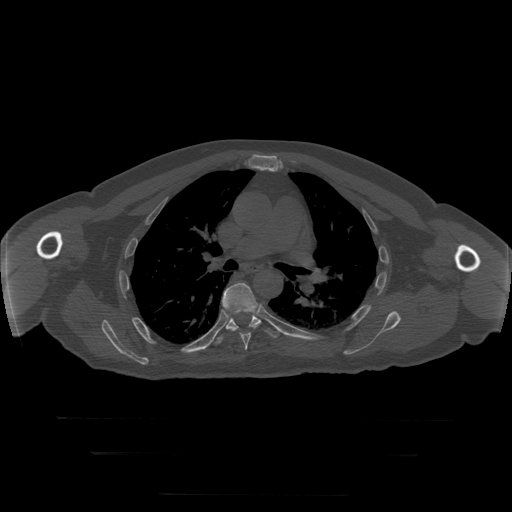
CT including the spine, one axial slice. Reconstruction kernel STANDARD. 120 kVp. Bone window (W 1800 / L 400 HU). 1.25 mm slice thickness. 512 × 512 image matrix. Patient age 73 years. From the clinical record (not read from this slice): primary cancer: prostate.
Annotated regions visible in this slice (semi-automatic segmentation, software-assisted and operator-edited):
- T6 vertebra: bounding box [x1, y1, x2, y2] px = [222, 283, 258, 351]
- T7 vertebra: [212, 313, 281, 344]